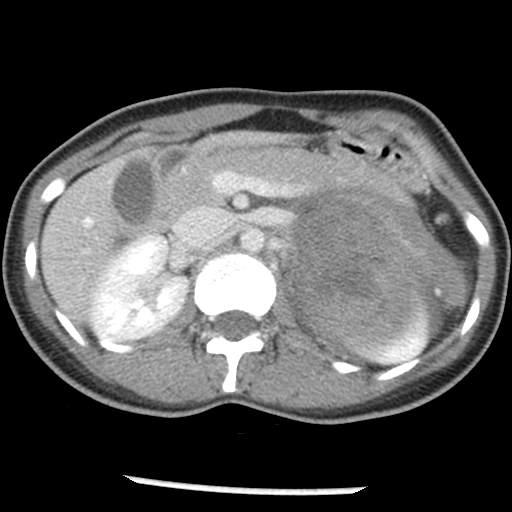
Contrast-enhanced abdominal CT, one axial slice. Slice 26 of 54 in the series (ordered by position). Reconstruction kernel STANDARD. 120 kVp. Intravenous contrast given. Soft-tissue window (W 400 / L 40 HU). 5 mm slice thickness. 512 × 512 image matrix, field of view 240 × 240 mm. Female patient, age 33 years. Case-level facts recorded for this patient, not image findings: diagnosis: adrenocortical carcinoma; tumour side: left adrenal; tumour size at pathology: 11 cm; Ki-67 index: 20 %; stage (as recorded): 2.
Outlined on this slice (semi-automatic segmentation, software-assisted and operator-edited):
- mass: bounding box <284,191,465,343> (left, top, right, bottom; pixels)